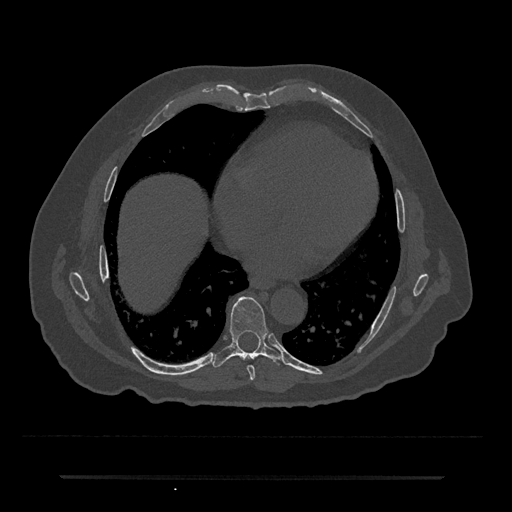
CT including the spine, one axial slice. Position 344 of 797 along the scan axis. Reconstruction kernel Br40s/3. Bone window (W 1800 / L 400 HU). 0.5 mm slice thickness. 512 × 512 image matrix. Patient: male, 69 years. Case-level facts recorded for this patient, not image findings: primary cancer: prostate.
Annotated regions visible in this slice (semi-automatically segmented with operator editing):
- T7 vertebra: bounding box (x1, y1, x2, y2) in pixels: (247, 365, 255, 381)
- T8 vertebra: (212, 297, 281, 368)